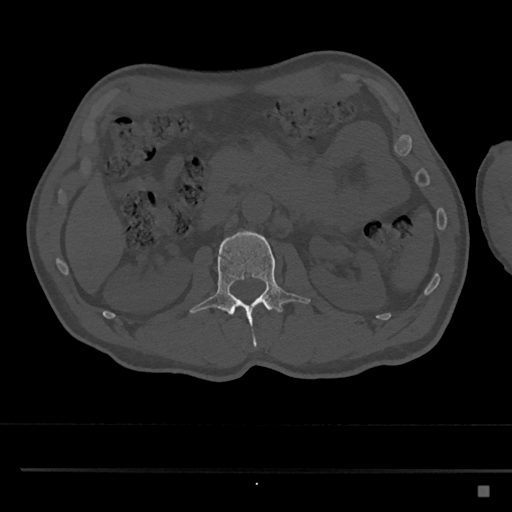
CT including the spine, one axial slice. Position 767 of 797 along the scan axis. Bone window (W 1800 / L 400 HU). 512 × 512 image matrix. Male patient, age 59 years. Case-level facts recorded for this patient, not image findings: primary cancer: prostate.
Annotated regions visible in this slice (semi-automatic segmentation, software-assisted and operator-edited):
- L2 vertebra: bounding box (x1, y1, x2, y2) in pixels: (190, 230, 311, 350)